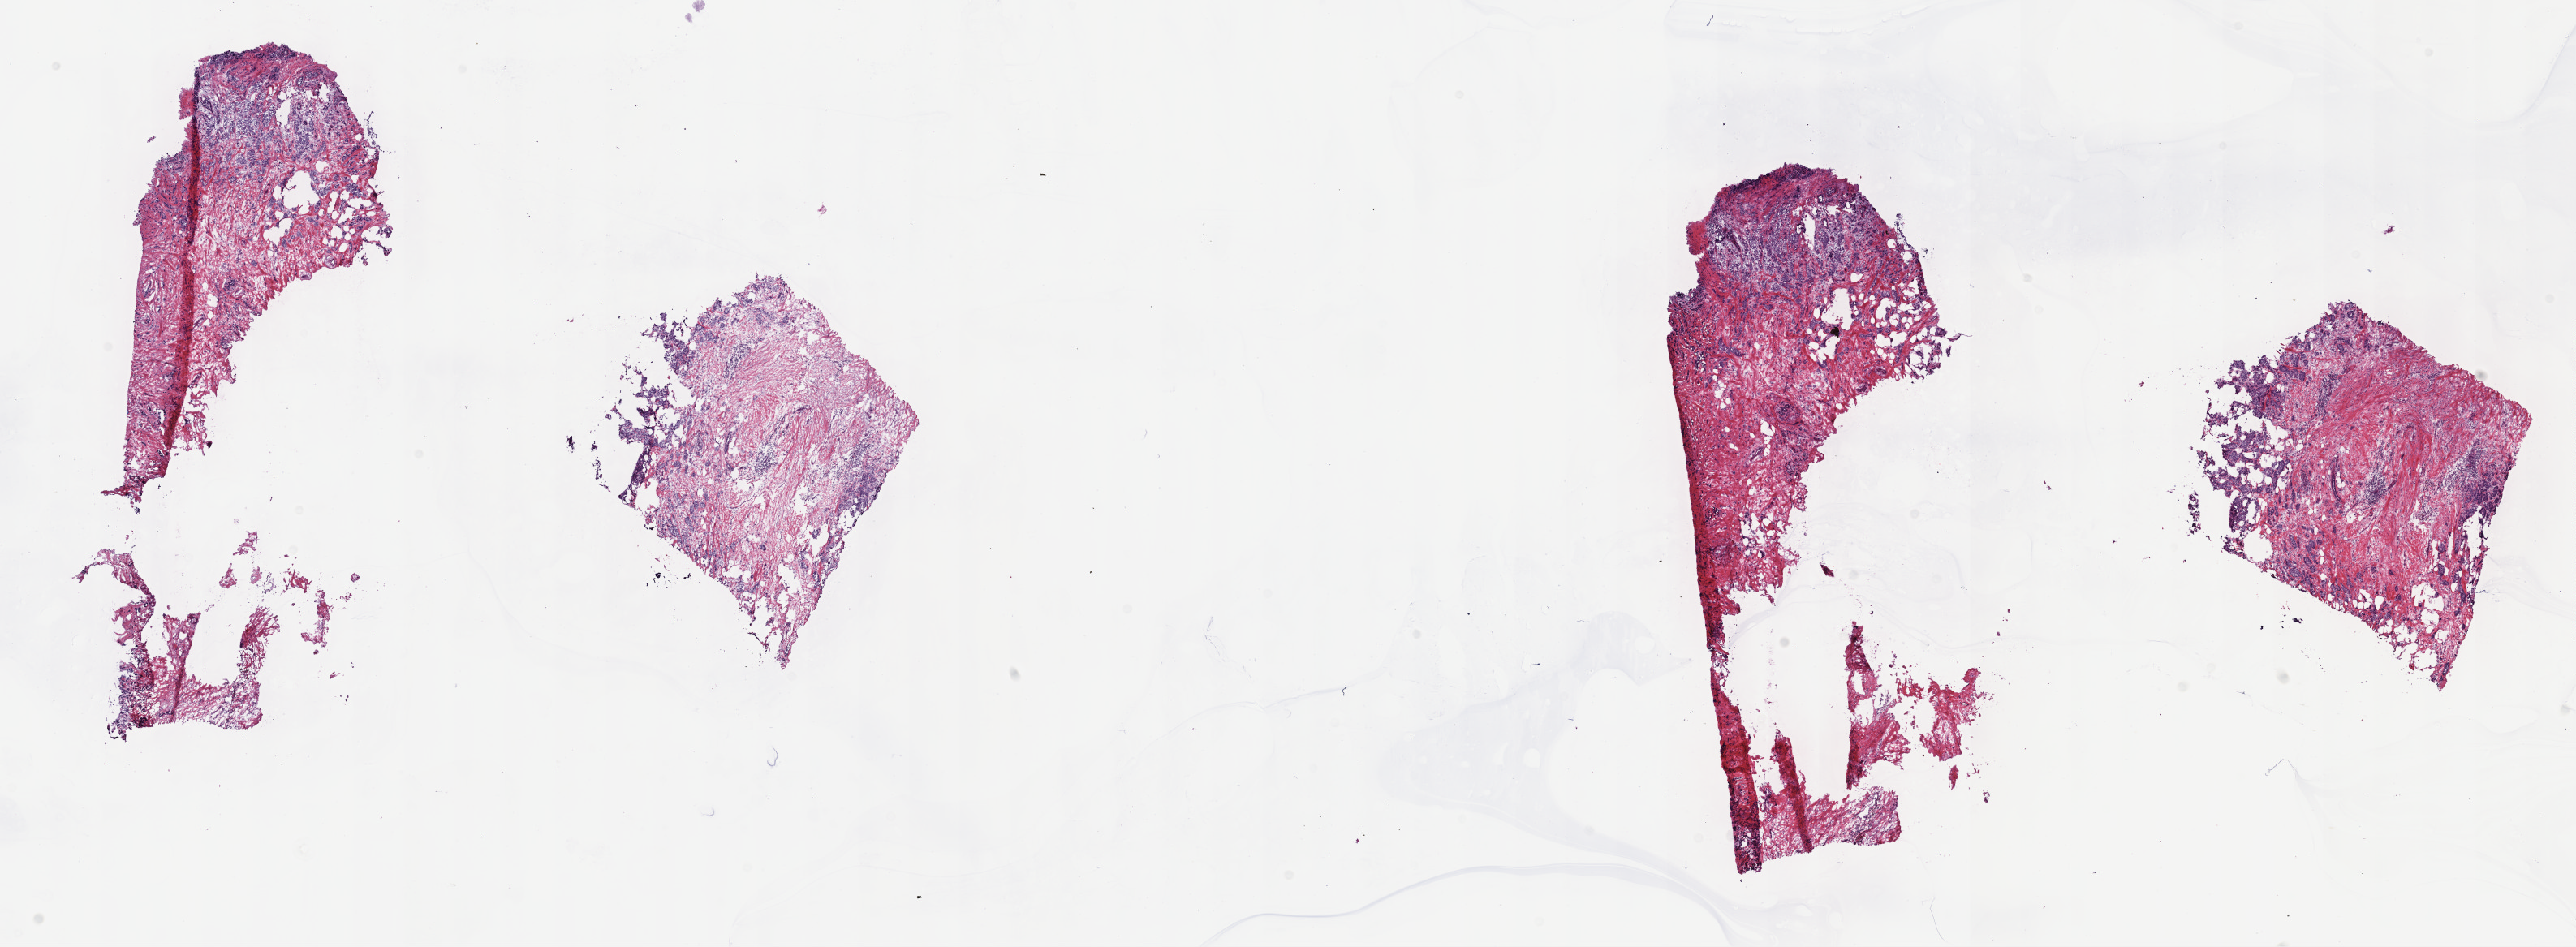
Whole-slide histology image, H&E — shown as a low-resolution overview of the whole scanned area (about 25.7 x 9.4 mm), frozen section from the top of the tissue portion, primary tumour sample from the breast. Female, age 72 years at initial diagnosis. Pathologist review of this section (percent, as recorded): tumour cells 22%, tumour nuclei 70%, normal cells 5%, stromal cells 73%, necrosis 0%. Inflammatory infiltration, as recorded: lymphocyte infiltration 10%, monocyte infiltration 1%, neutrophil infiltration 2%.
Histologic diagnosis: Infiltrating duct carcinoma, NOS. AJCC pathologic stage: IA (7th edition).